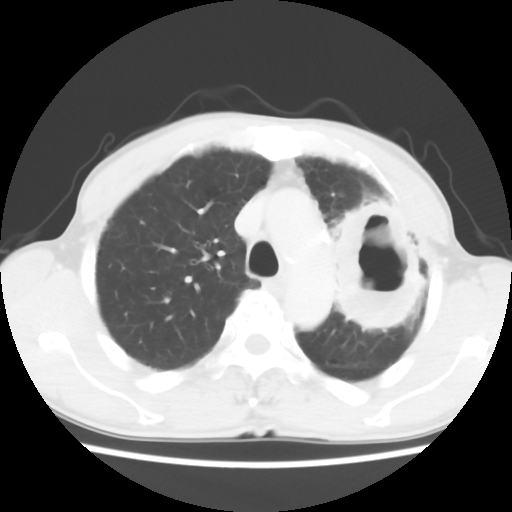
Chest CT, one axial slice; position 44 of 60 along the scan axis; lung window (W 1500 / L -600 HU); 512 × 512 image matrix, field of view 308 × 308 mm. Male patient, age 64 years. Case-level facts recorded for this patient, not image findings: clinical TNM (as recorded): T3 N3 M0; histopathological grade: G3.
Structures marked on this image (rectangle marked by the reading radiologist):
- lung tumour (recorded histology: adenocarcinoma): bounding box [x1, y1, x2, y2] px = [323, 191, 428, 342]